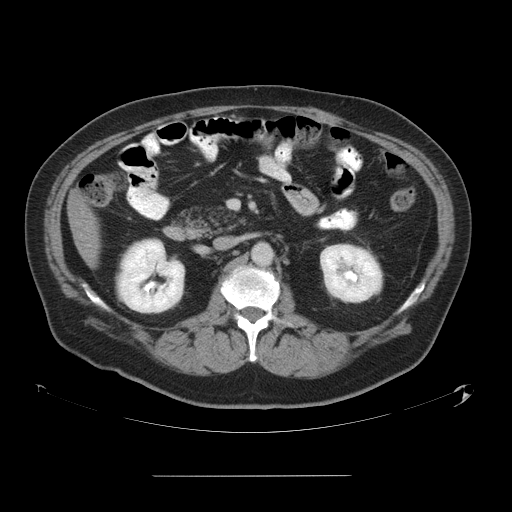
Contrast-enhanced abdominal CT, one axial slice; slice 21 of 58 in the series (ordered by position); intravenous contrast given; soft-tissue window (W 400 / L 40 HU); 512 × 512 image matrix, field of view 480 × 480 mm. Male patient, age 63 years. Case-level facts recorded for this patient, not image findings: diagnosis: colorectal cancer liver metastases, imaged before liver resection; multiple liver metastases: no; largest metastasis: 4.2 cm; disease in both lobes: no.
Outlined on this slice (manually delineated by an expert):
- liver: box from (x=71, y=193) to (x=99, y=264) px
- planned liver remnant (the part of the liver to remain after resection): (x=71, y=193)–(x=99, y=264)